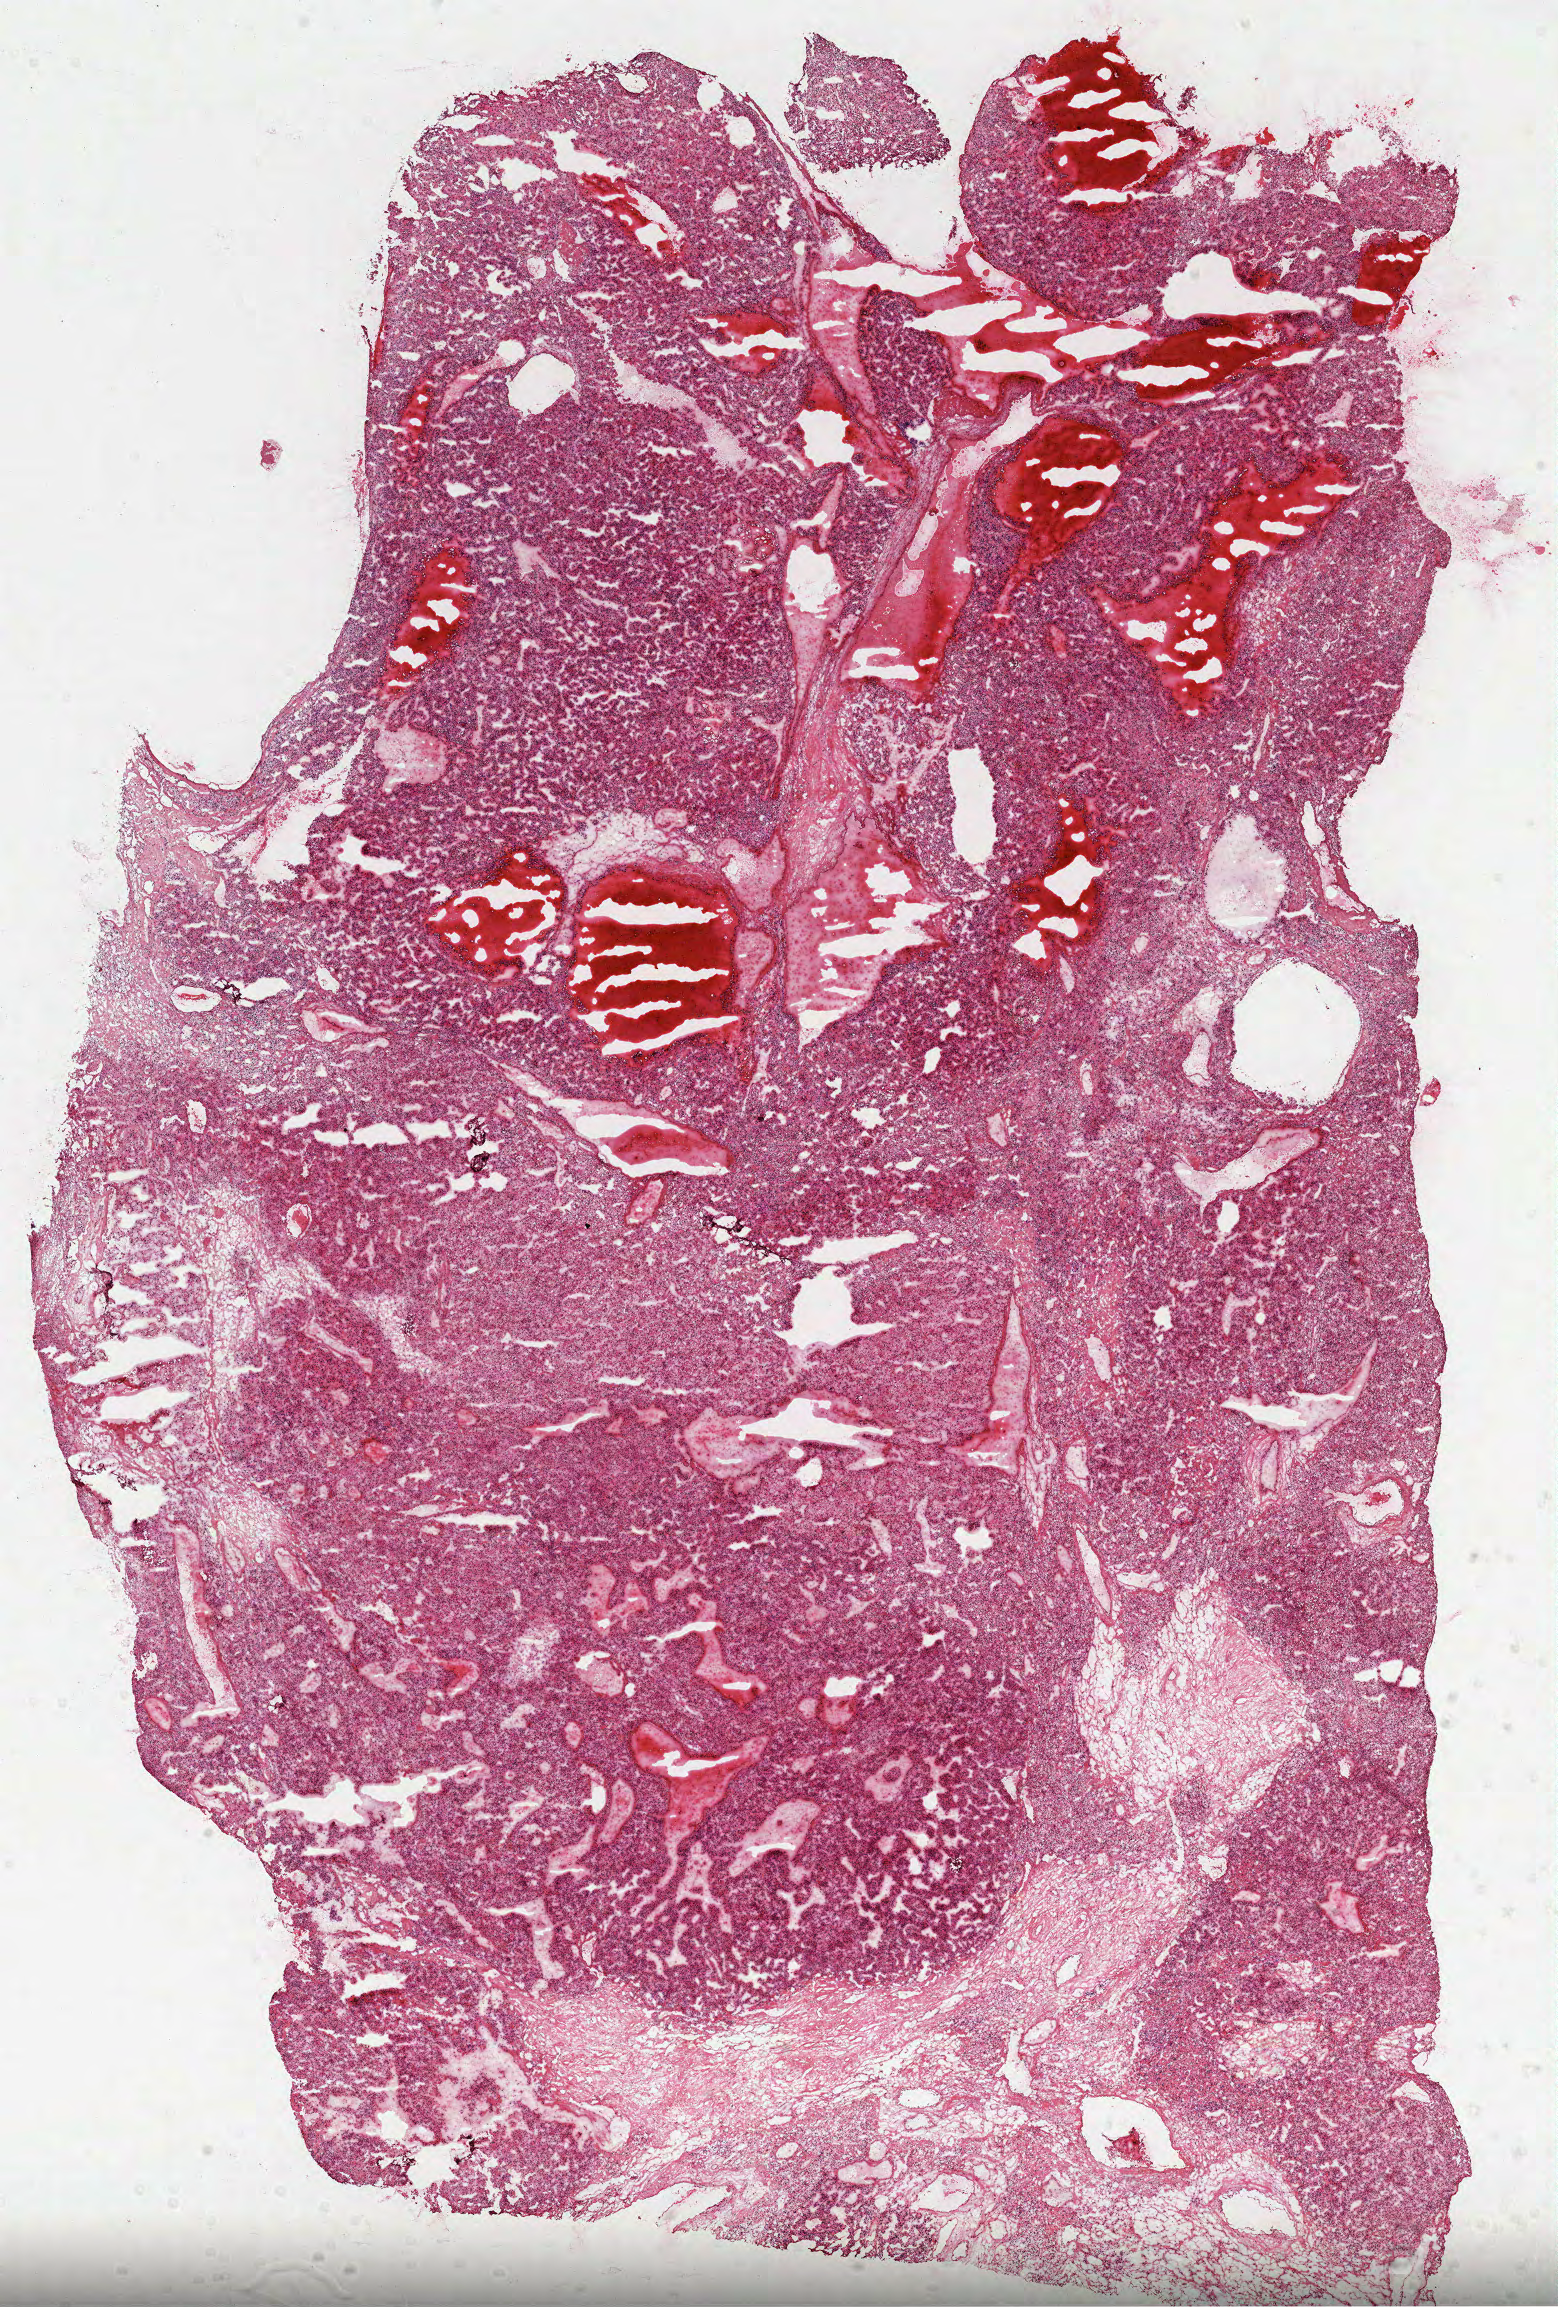
H&E whole-slide image, a low-resolution overview of the entire scanned area, about 12.6 x 18.6 mm. Formalin-fixed paraffin-embedded (FFPE) diagnostic section. Primary tumour sample from the kidney. Male patient; age at initial diagnosis 63 years.
Histologic diagnosis: Clear cell adenocarcinoma, NOS.